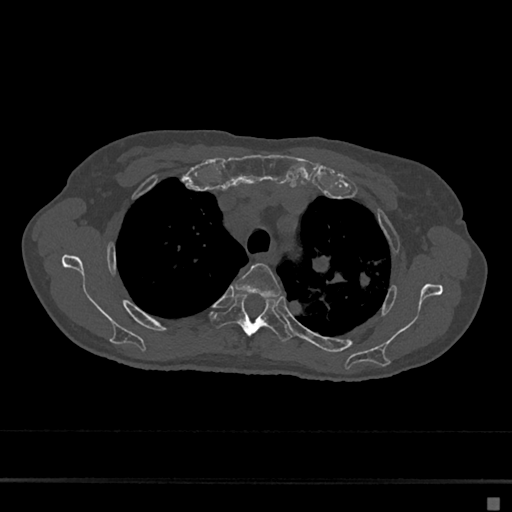
CT including the spine, one axial slice. Slice 515 of 797 in the series (ordered by position). 120 kVp. Bone window (W 1800 / L 400 HU). 0.5 mm slice thickness. 512 × 512 image matrix, field of view 360 × 360 mm. Female patient, age 68 years. From the clinical record (not read from this slice): primary cancer: renal.
Annotated regions visible in this slice (semi-automatic segmentation, software-assisted and operator-edited):
- T3 vertebra: box from (x=236, y=263) to (x=281, y=299) px
- T4 vertebra: (x=211, y=295)–(x=291, y=341)